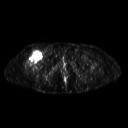
FDG PET of an extremity soft-tissue mass (from a PET/CT study), one axial slice; slice 279 of 311 in the series (ordered by position); 3.27 mm slice thickness; 128 × 128 image matrix, field of view 500 × 500 mm. Female patient, age 57 years. Case-level facts recorded for this patient, not image findings: histological type: pleiomorphic undifferentiated sarcoma; grade: high; site of the primary tumour: right quadricep.
Annotated regions visible in this slice (expert contour drawn on MRI and transferred to this co-registered scan by the dataset authors):
- tumour plus oedema (research contour): box from (x=25, y=50) to (x=43, y=68) px
- tumour (research contour): (x=25, y=50)–(x=43, y=68)